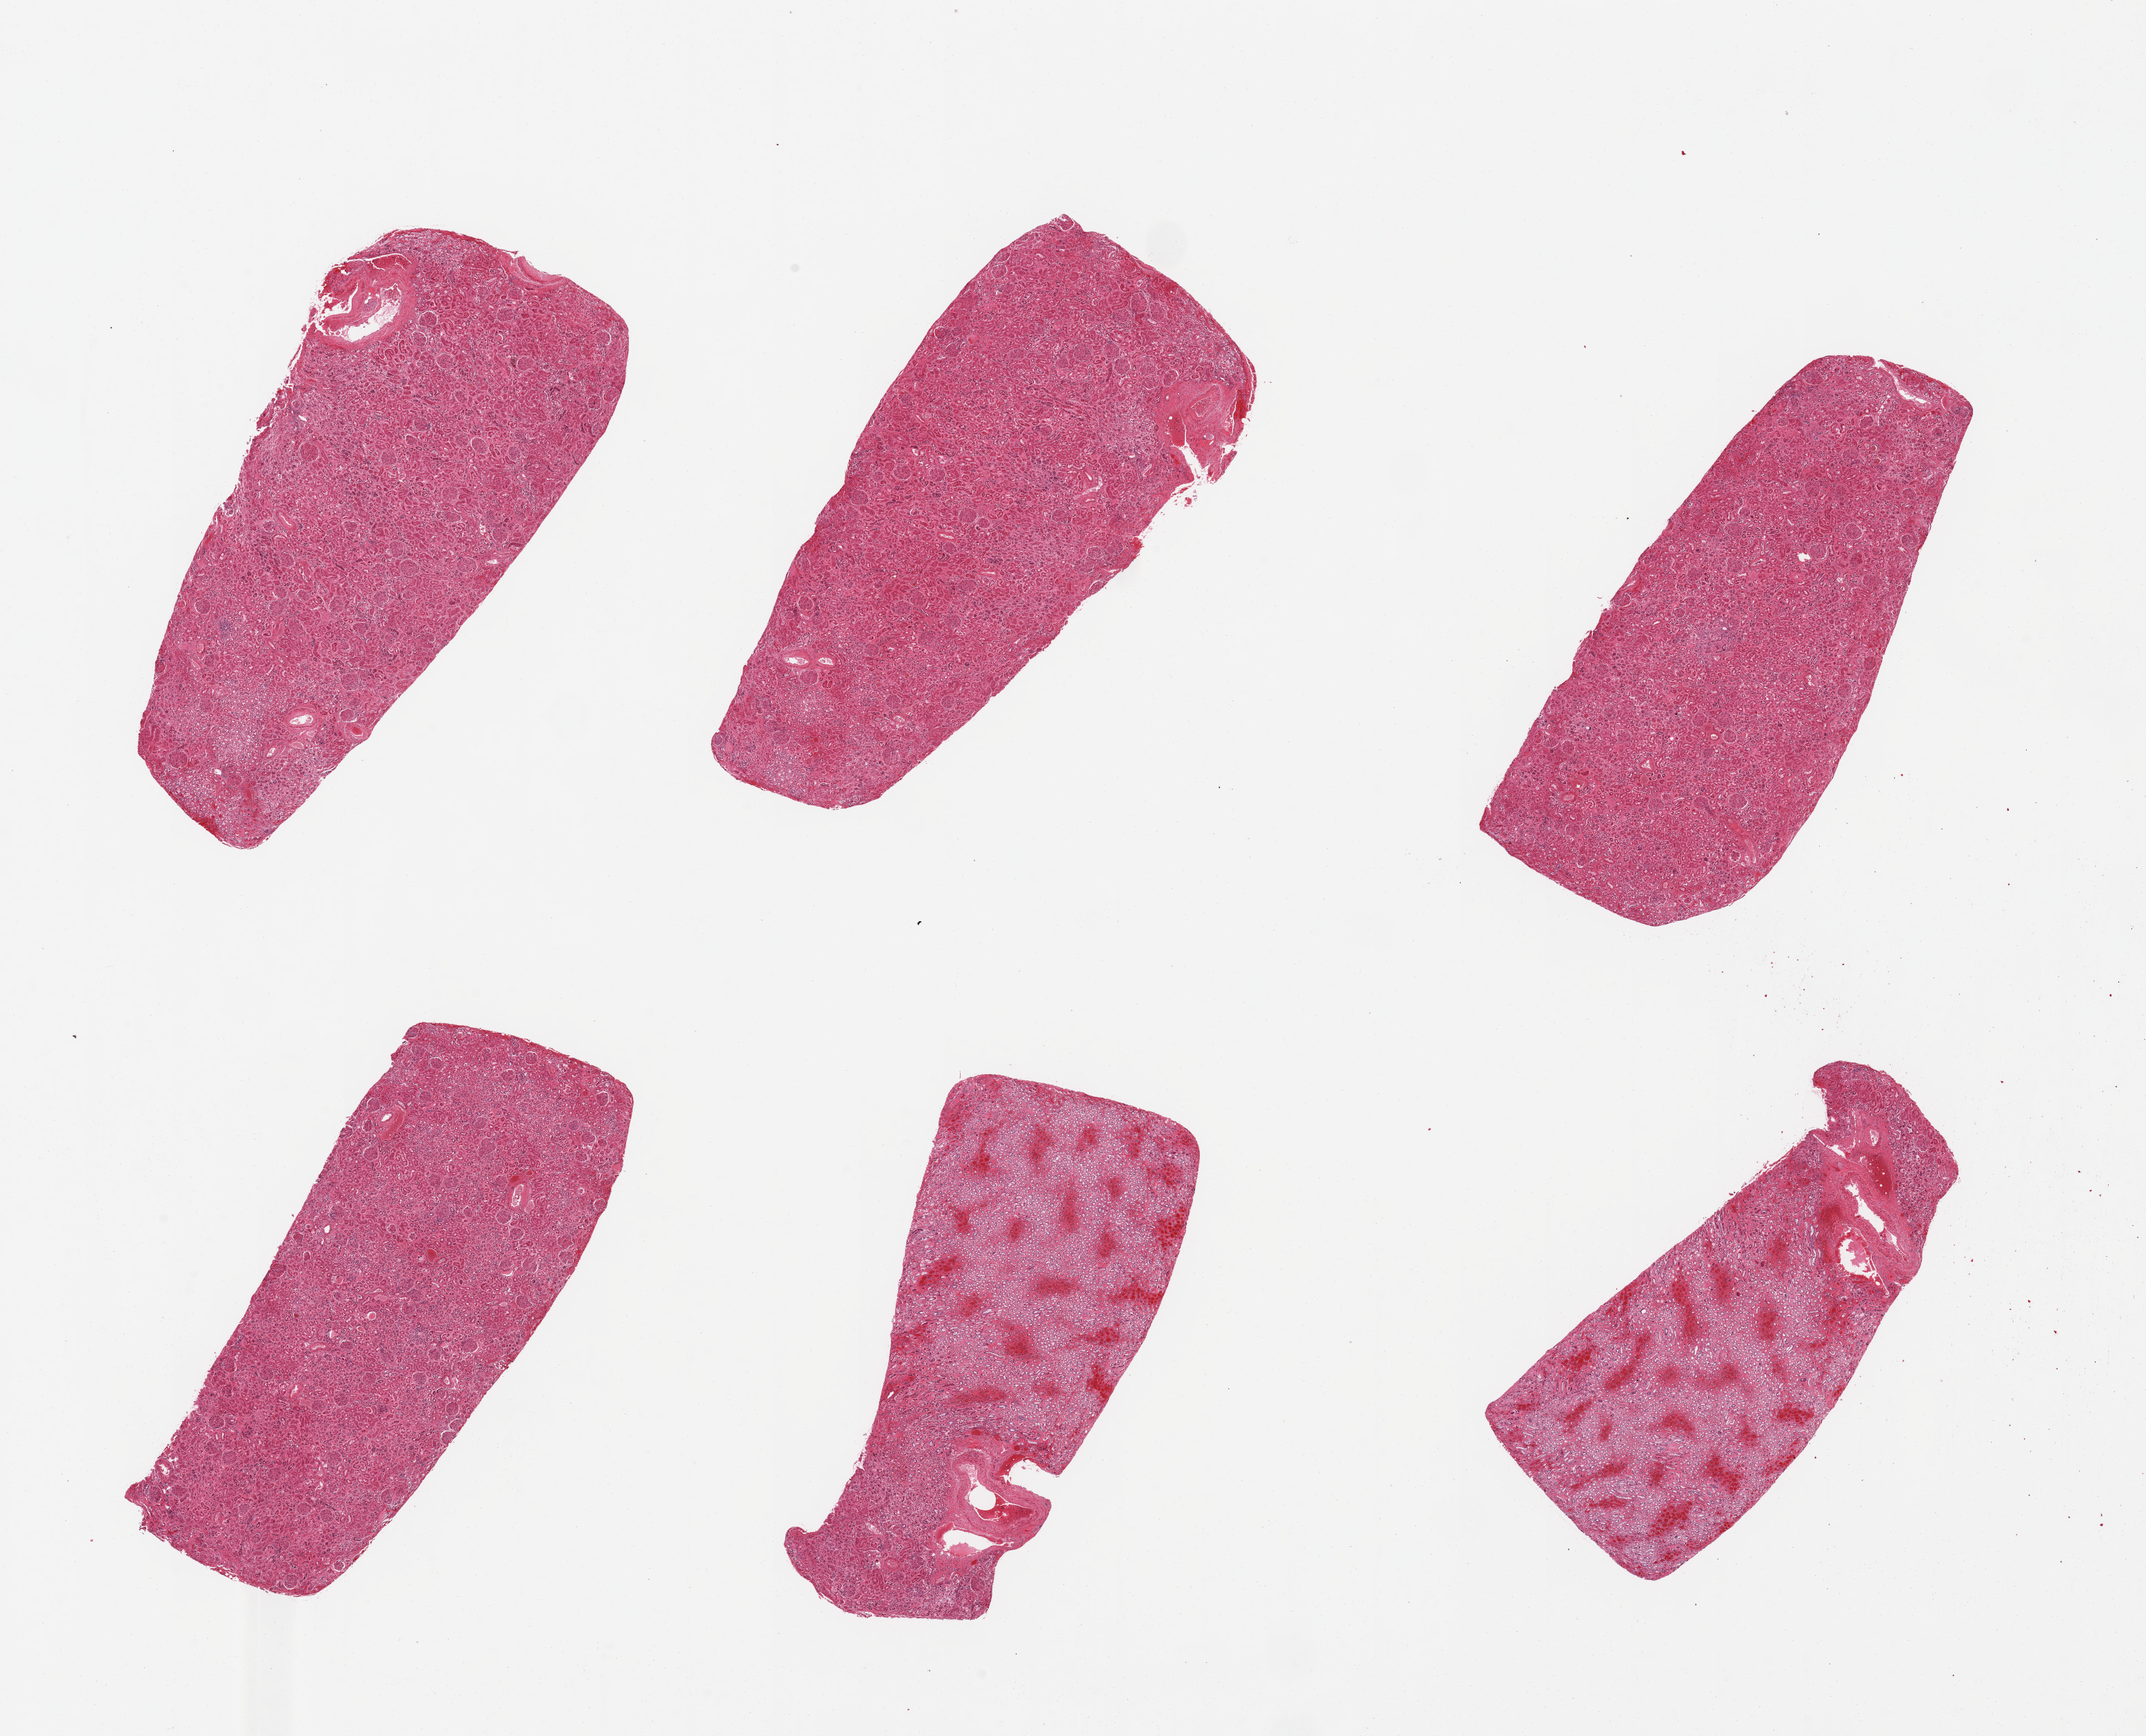
H&E whole-slide image, a low-resolution overview of the entire scanned area, about 24.6 x 19.9 mm; PAXgene-fixed, paraffin-embedded tissue; target tissue: renal cortex; tissue donor sample.
- review note (as recorded): 6 pieces; 2 pieces are mostly medulla